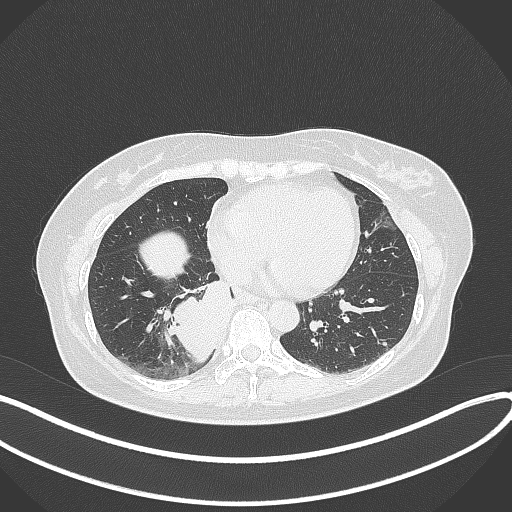
Chest CT, one axial slice. Position 125 of 331 along the scan axis. 120 kVp. Lung window (W 1500 / L -600 HU). 512 × 512 image matrix. Female patient, age 54 years. From the clinical record (not read from this slice): clinical TNM (as recorded): T4 N0 M0.
Structures marked on this image (rectangle marked by the reading radiologist):
- lung tumour (recorded histology: adenocarcinoma): box from (x=166, y=280) to (x=239, y=378) px